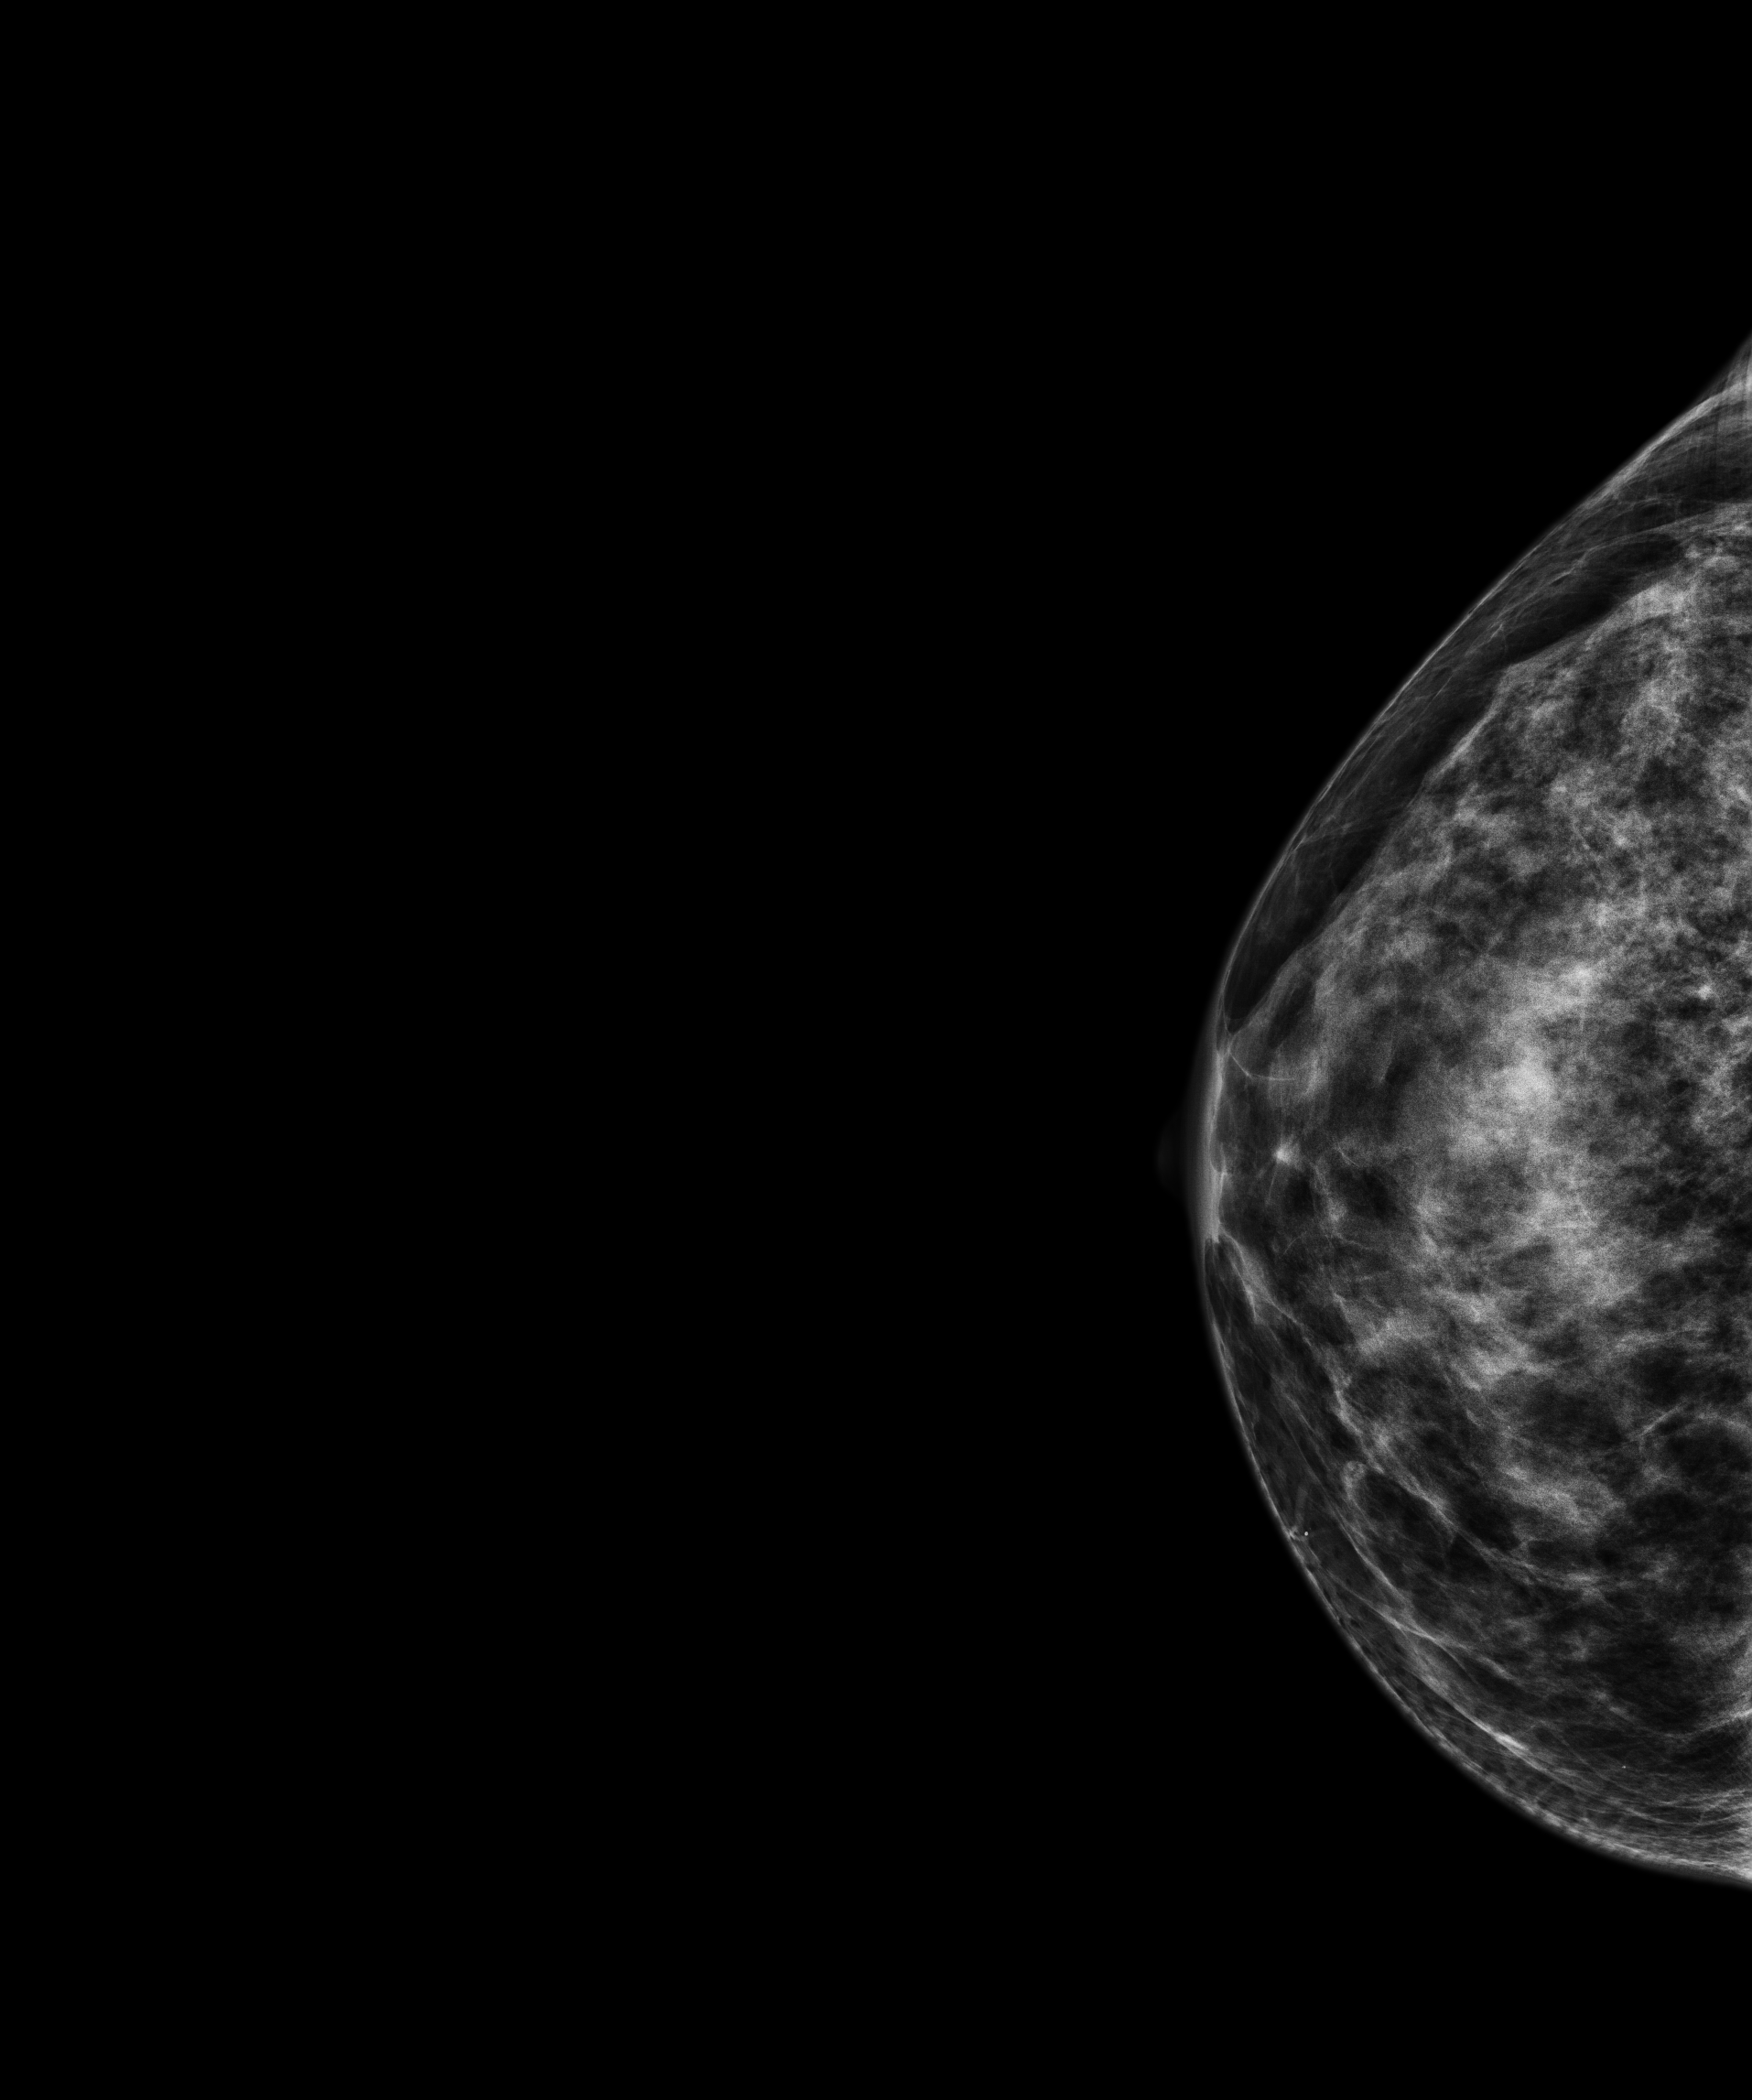
Annual screening mammography examination. Patient: female, 44 years.
Image type: full-field digital mammogram. Breast: right. Projection: CC view.